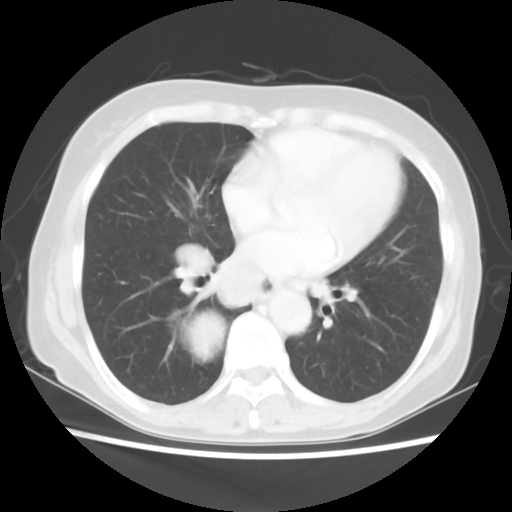
Chest CT, one axial slice. Position 23 of 56 along the scan axis. Reconstruction kernel STANDARD. Lung window (W 1500 / L -600 HU). 512 × 512 image matrix, field of view 332 × 332 mm. Female patient, age 66 years. From the clinical record (not read from this slice): clinical TNM (as recorded): T2 N3 M0; histopathological grade: G3.
Structures marked on this image (bounding box drawn by a radiologist):
- lung tumour (recorded histology: small cell carcinoma): box from (x=189, y=305) to (x=223, y=362) px